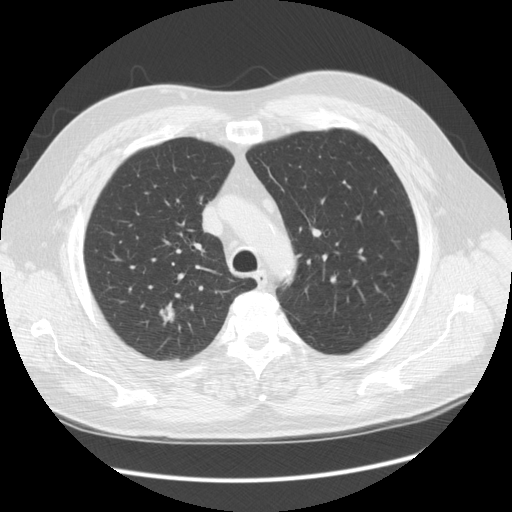
Low-dose screening chest CT, one axial slice. Slice 82 of 108 in the series (ordered by position). 120 kVp. Lung window (W 1500 / L -600 HU). 2.5 mm slice thickness. 512 × 512 image matrix, field of view 380 × 380 mm.
Outlined on this slice (expert manual segmentation):
- lesion 1 (tumor, upper lobe of right lung): bounding box <159,302,175,325> (left, top, right, bottom; pixels)